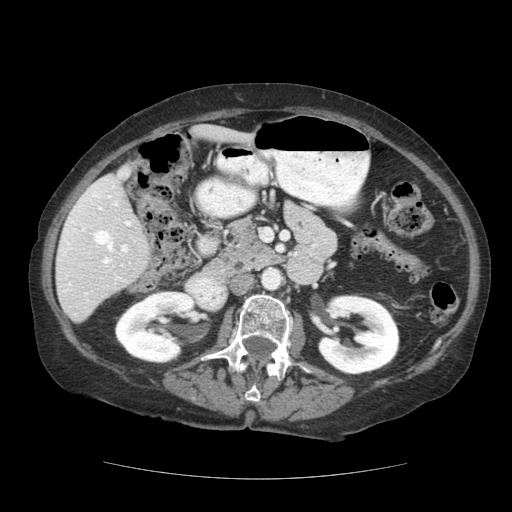
Contrast-enhanced abdominal CT (liver protocol), one axial slice; 140 kVp; soft-tissue window (W 400 / L 40 HU); 2.5 mm slice thickness; 512 × 512 image matrix. From the clinical record (not read from this slice): diagnosis: hepatocellular carcinoma (patient treated with transarterial chemoembolisation; whether this scan precedes or follows treatment is not stated here); TNM stage (as recorded): Stage-I; Child-Pugh class: A; tumour differentiation: moderately-poorly differentiated; tumour nodularity: uninodular.
Outlined on this slice (semi-automatically segmented with operator editing):
- liver parenchyma outside the tumour (the mass and vessels are separate outlines, so this box may not span the whole liver): box from (x=56, y=126) to (x=254, y=322) px
- liver vessels: (x=60, y=173)–(x=131, y=295)